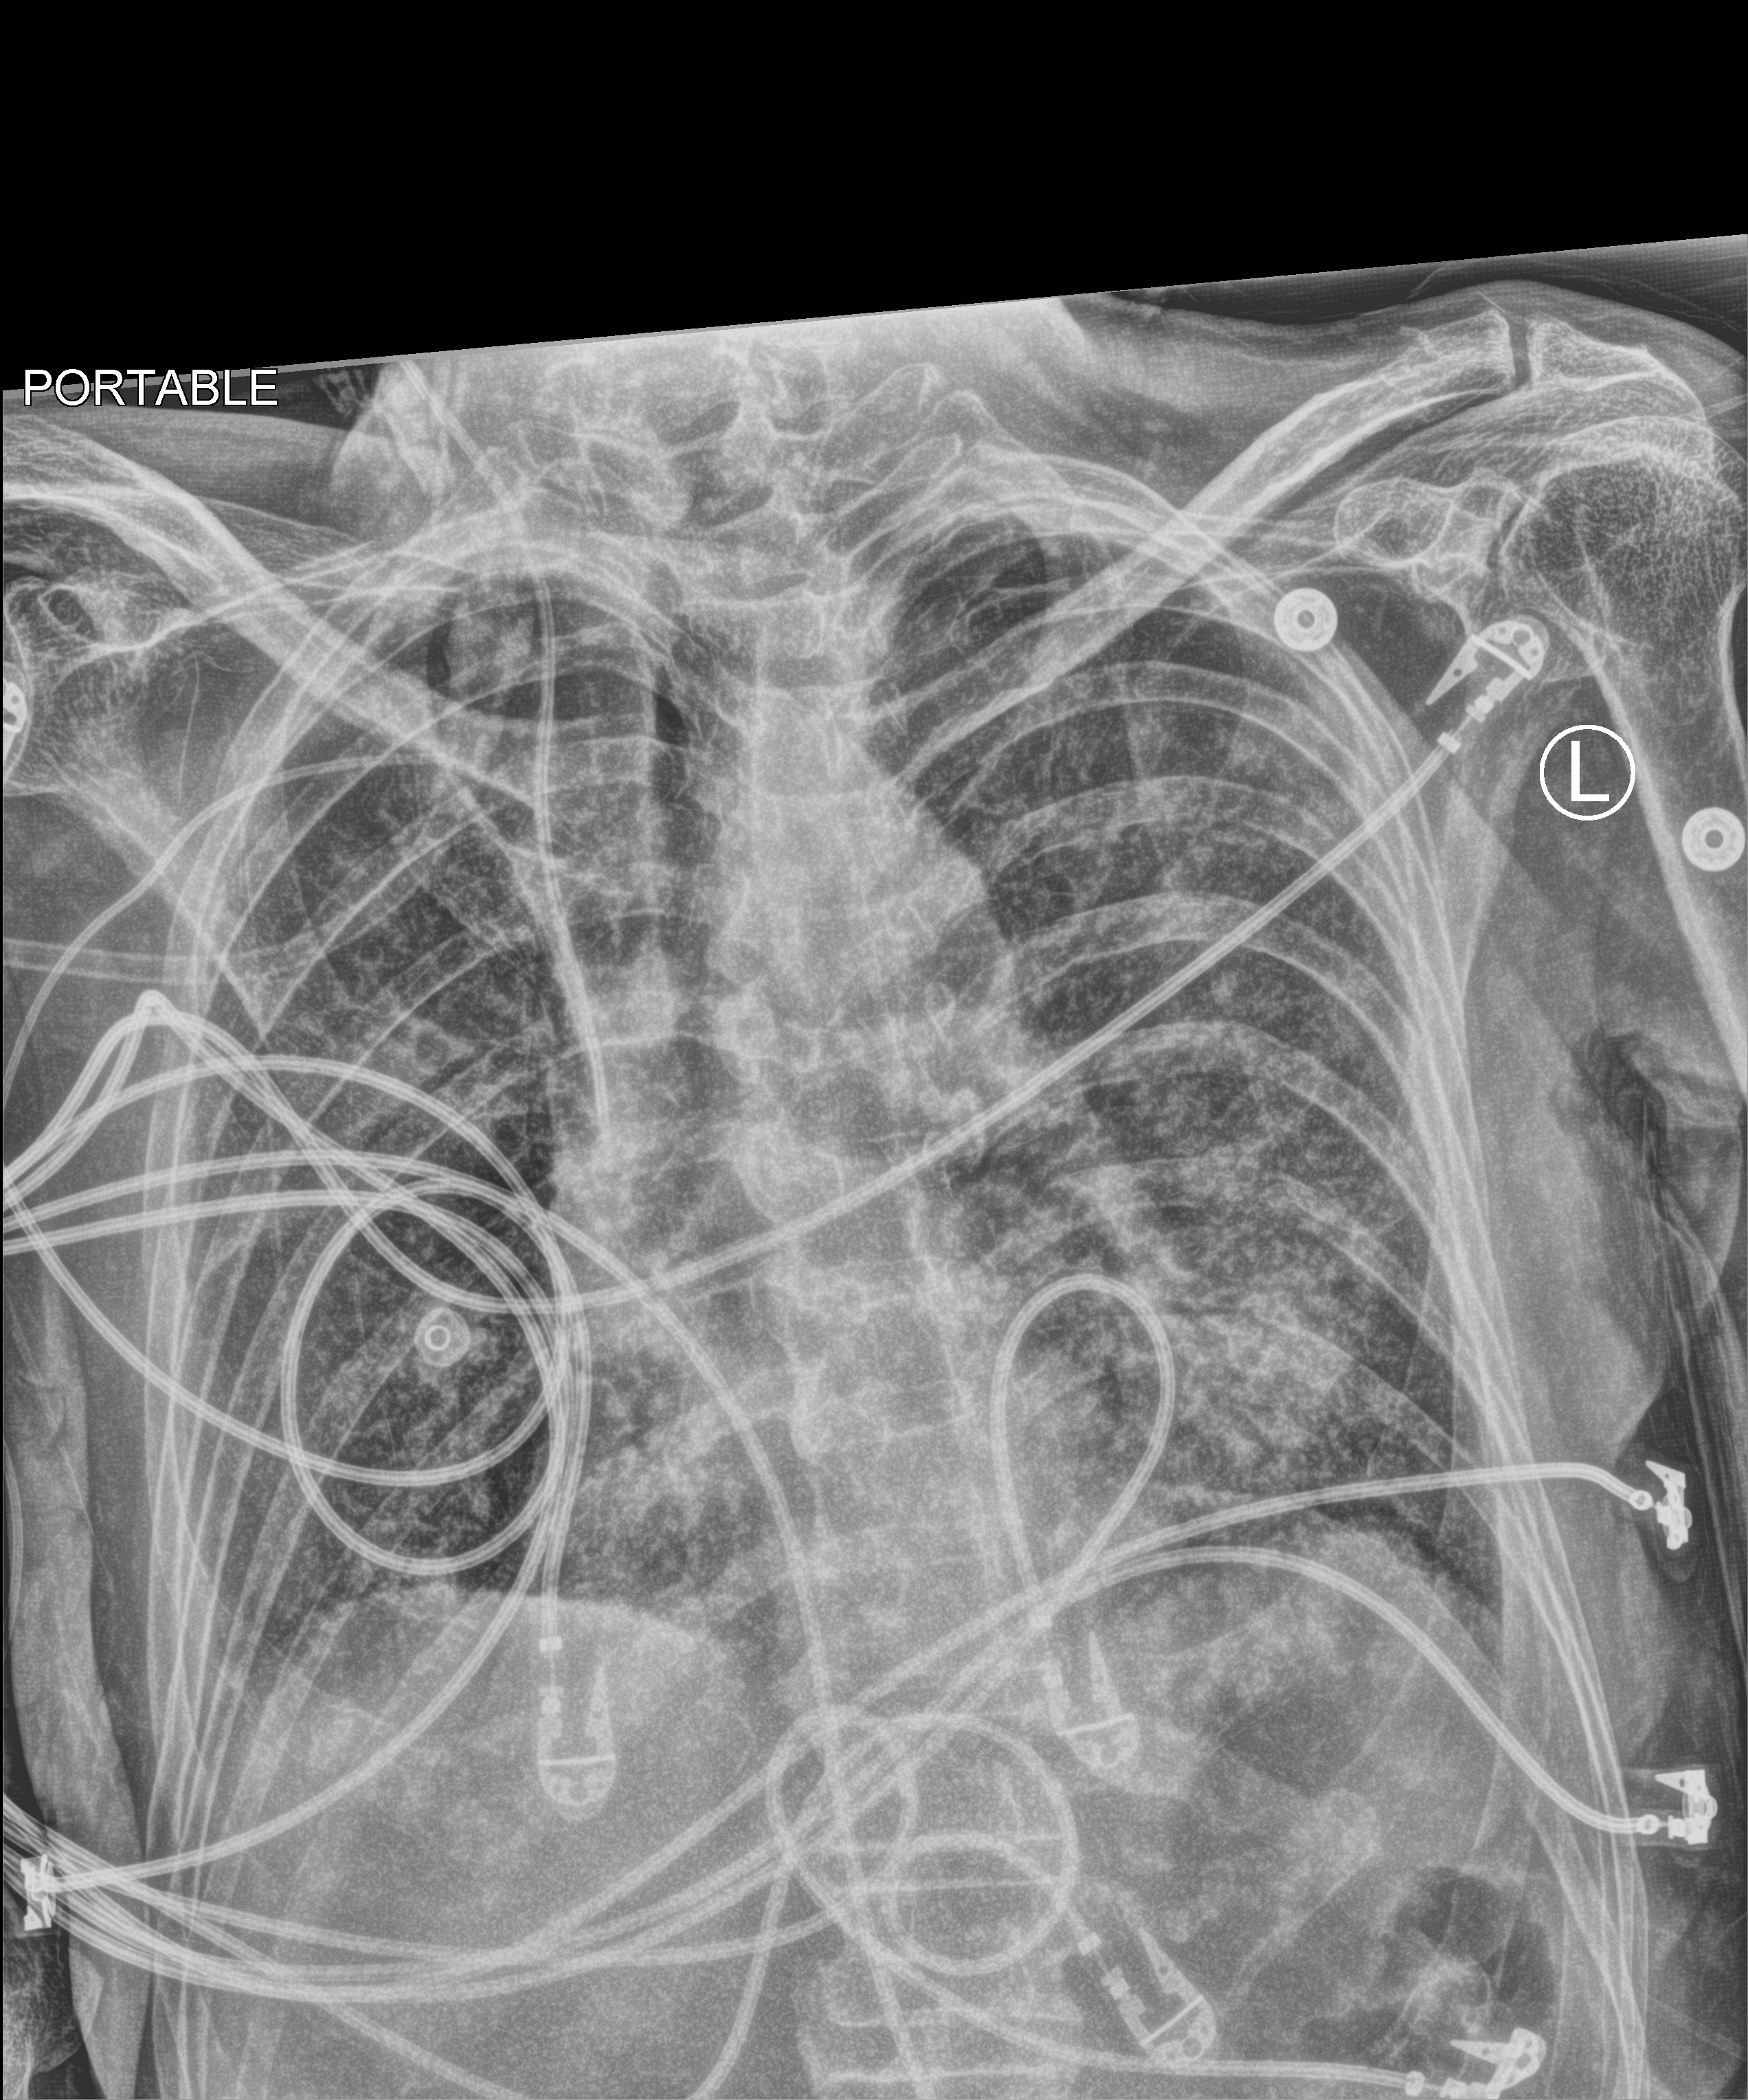
Portable chest radiograph, anteroposterior (AP) projection. Patient hospitalised with COVID-19; male, aged 60–74 years.
Hospital-stay facts (about this admission, not read from this image; timing relative to this image not recorded): hypertension (admission record): yes; admitted to intensive care during this hospital stay: yes.